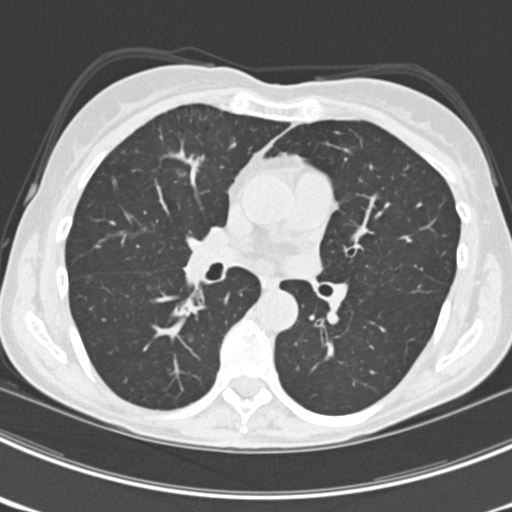
Low-dose screening chest CT, axial slice, third annual screen, lung window (W 1500 / L -600 HU), 2 mm slice thickness, slice 96 of 225 in the series. Female, age 63 years at enrolment.
Lesion marked by an expert reader, bounding box <153,135,221,196> (left, top, right, bottom; pixels). The screening reader recorded 9 non-calcified nodules or masses ≥4 mm on this exam; which of them this box marks is not recorded. Official screen result: positive, other. Lung cancer was diagnosed 15 days after this screen: bronchiolo-alveolar adenocarcinoma, NOS, right upper lobe, right middle lobe, right lower lobe, left upper lobe, left lower lobe, moderately differentiated (G2), stage IV (AJCC 6th edition).